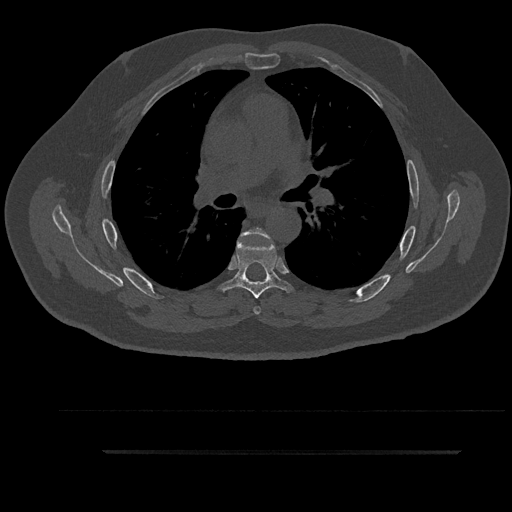
CT including the spine, one axial slice. Slice 588 of 797 in the series (ordered by position). Reconstruction kernel Br40s/3. 120 kVp. Bone window (W 1800 / L 400 HU). 0.5 mm slice thickness. 512 × 512 image matrix. Male patient, age 63 years. Case-level facts recorded for this patient, not image findings: primary cancer: renal.
Outlined on this slice (semi-automatic segmentation, software-assisted and operator-edited):
- T5 vertebra: bounding box <241,227,273,315> (left, top, right, bottom; pixels)
- T6 vertebra: <221,235,291,299>